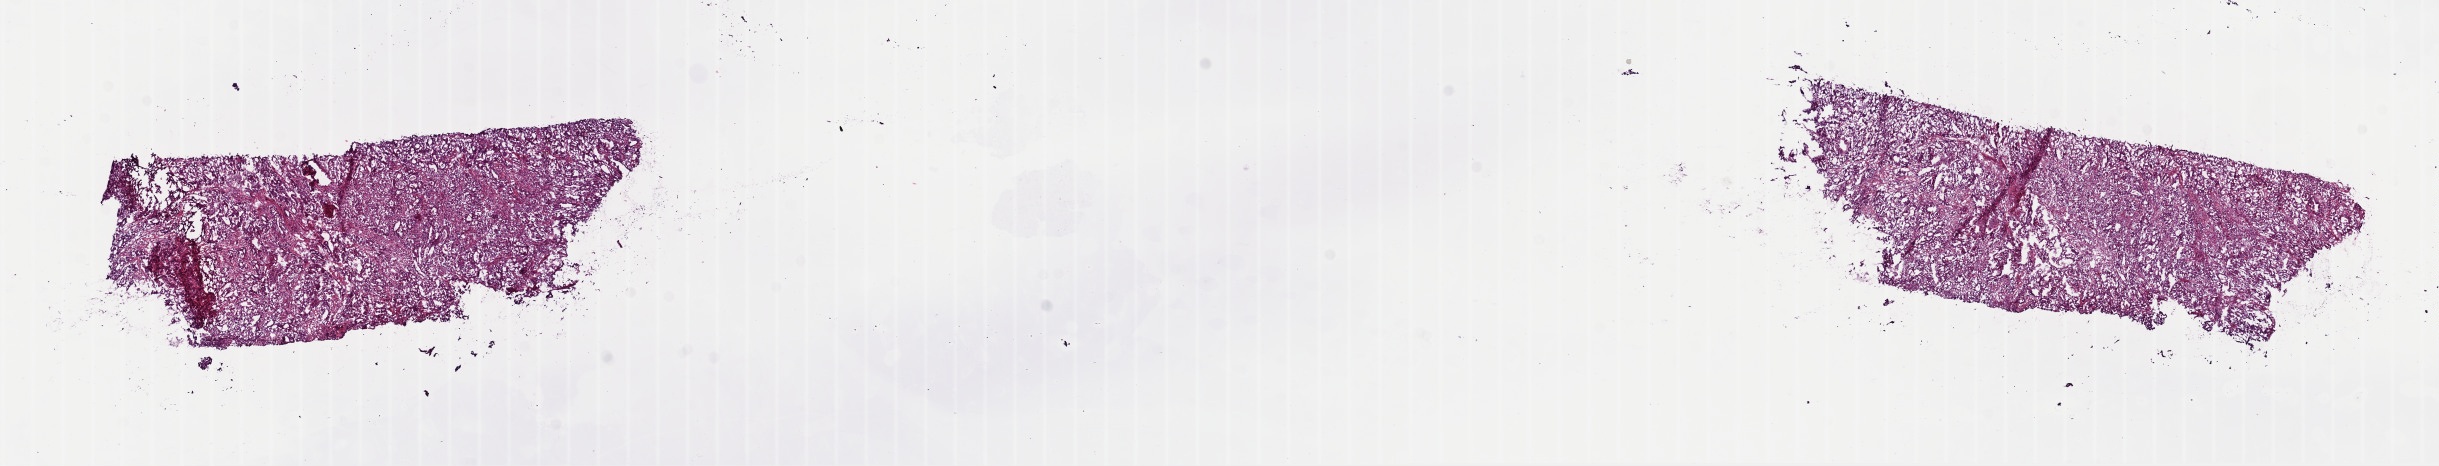
Hematoxylin and eosin (H&E) stained whole-slide image — whole scanned area (about 19.3 x 3.7 mm, slide scanned at 40x) shown as a low-resolution overview. Frozen section from the top of the tissue portion. Stomach, primary tumour sample. Female patient; age at initial diagnosis 68 years. Histologic grade: G2 (moderately differentiated). Slide review estimates, as recorded: tumour cells 60%, tumour nuclei 80%, normal cells 30%, stromal cells 10%, necrosis 0%. Inflammatory infiltration, as recorded: lymphocyte infiltration 0%, monocyte infiltration 0%, neutrophil infiltration 0%.
- AJCC pathologic stage: IB (7th edition)
- lymph nodes positive (case pathology): 0 of 14 examined
- pathologic diagnosis: Adenocarcinoma, NOS (cardia, NOS)